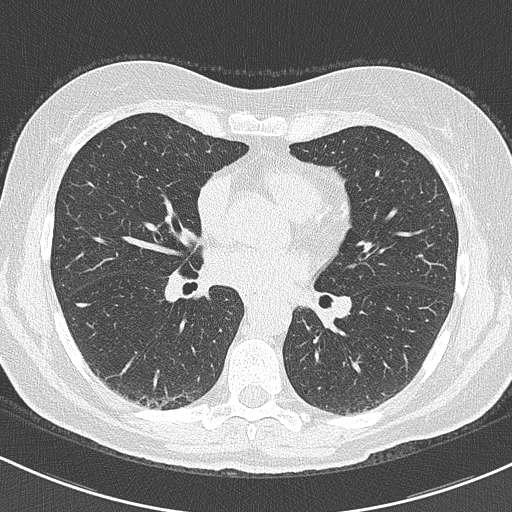
Low-dose screening chest CT, one axial slice. Position 102 of 201 along the scan axis. Lung window (W 1500 / L -600 HU). 512 × 512 image matrix, field of view 312 × 312 mm.
Outlined on this slice (manually delineated by an expert):
- lesion 1 (tumor, upper lobe of right lung): box from (x=76, y=303) to (x=91, y=308) px